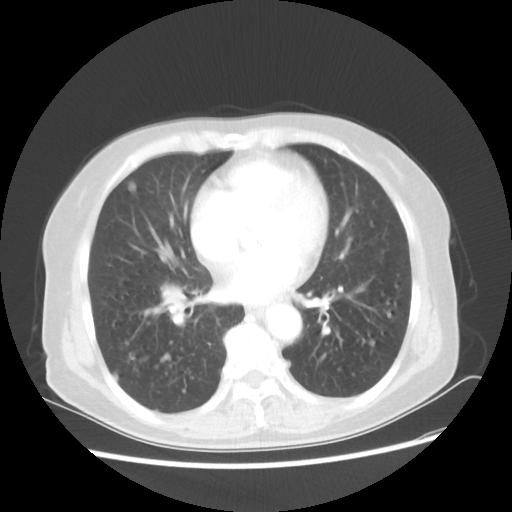
Chest CT, one axial slice. Position 24 of 56 along the scan axis. 80 kVp. Lung window (W 1500 / L -600 HU). 5 mm slice thickness. 512 × 512 image matrix, field of view 360 × 360 mm. Patient: female, 68 years. Case-level facts recorded for this patient, not image findings: clinical TNM (as recorded): T1c N3 M0.
Outlined on this slice (rectangle marked by the reading radiologist):
- lung tumour (recorded histology: squamous cell carcinoma): box from (x=148, y=276) to (x=204, y=318) px